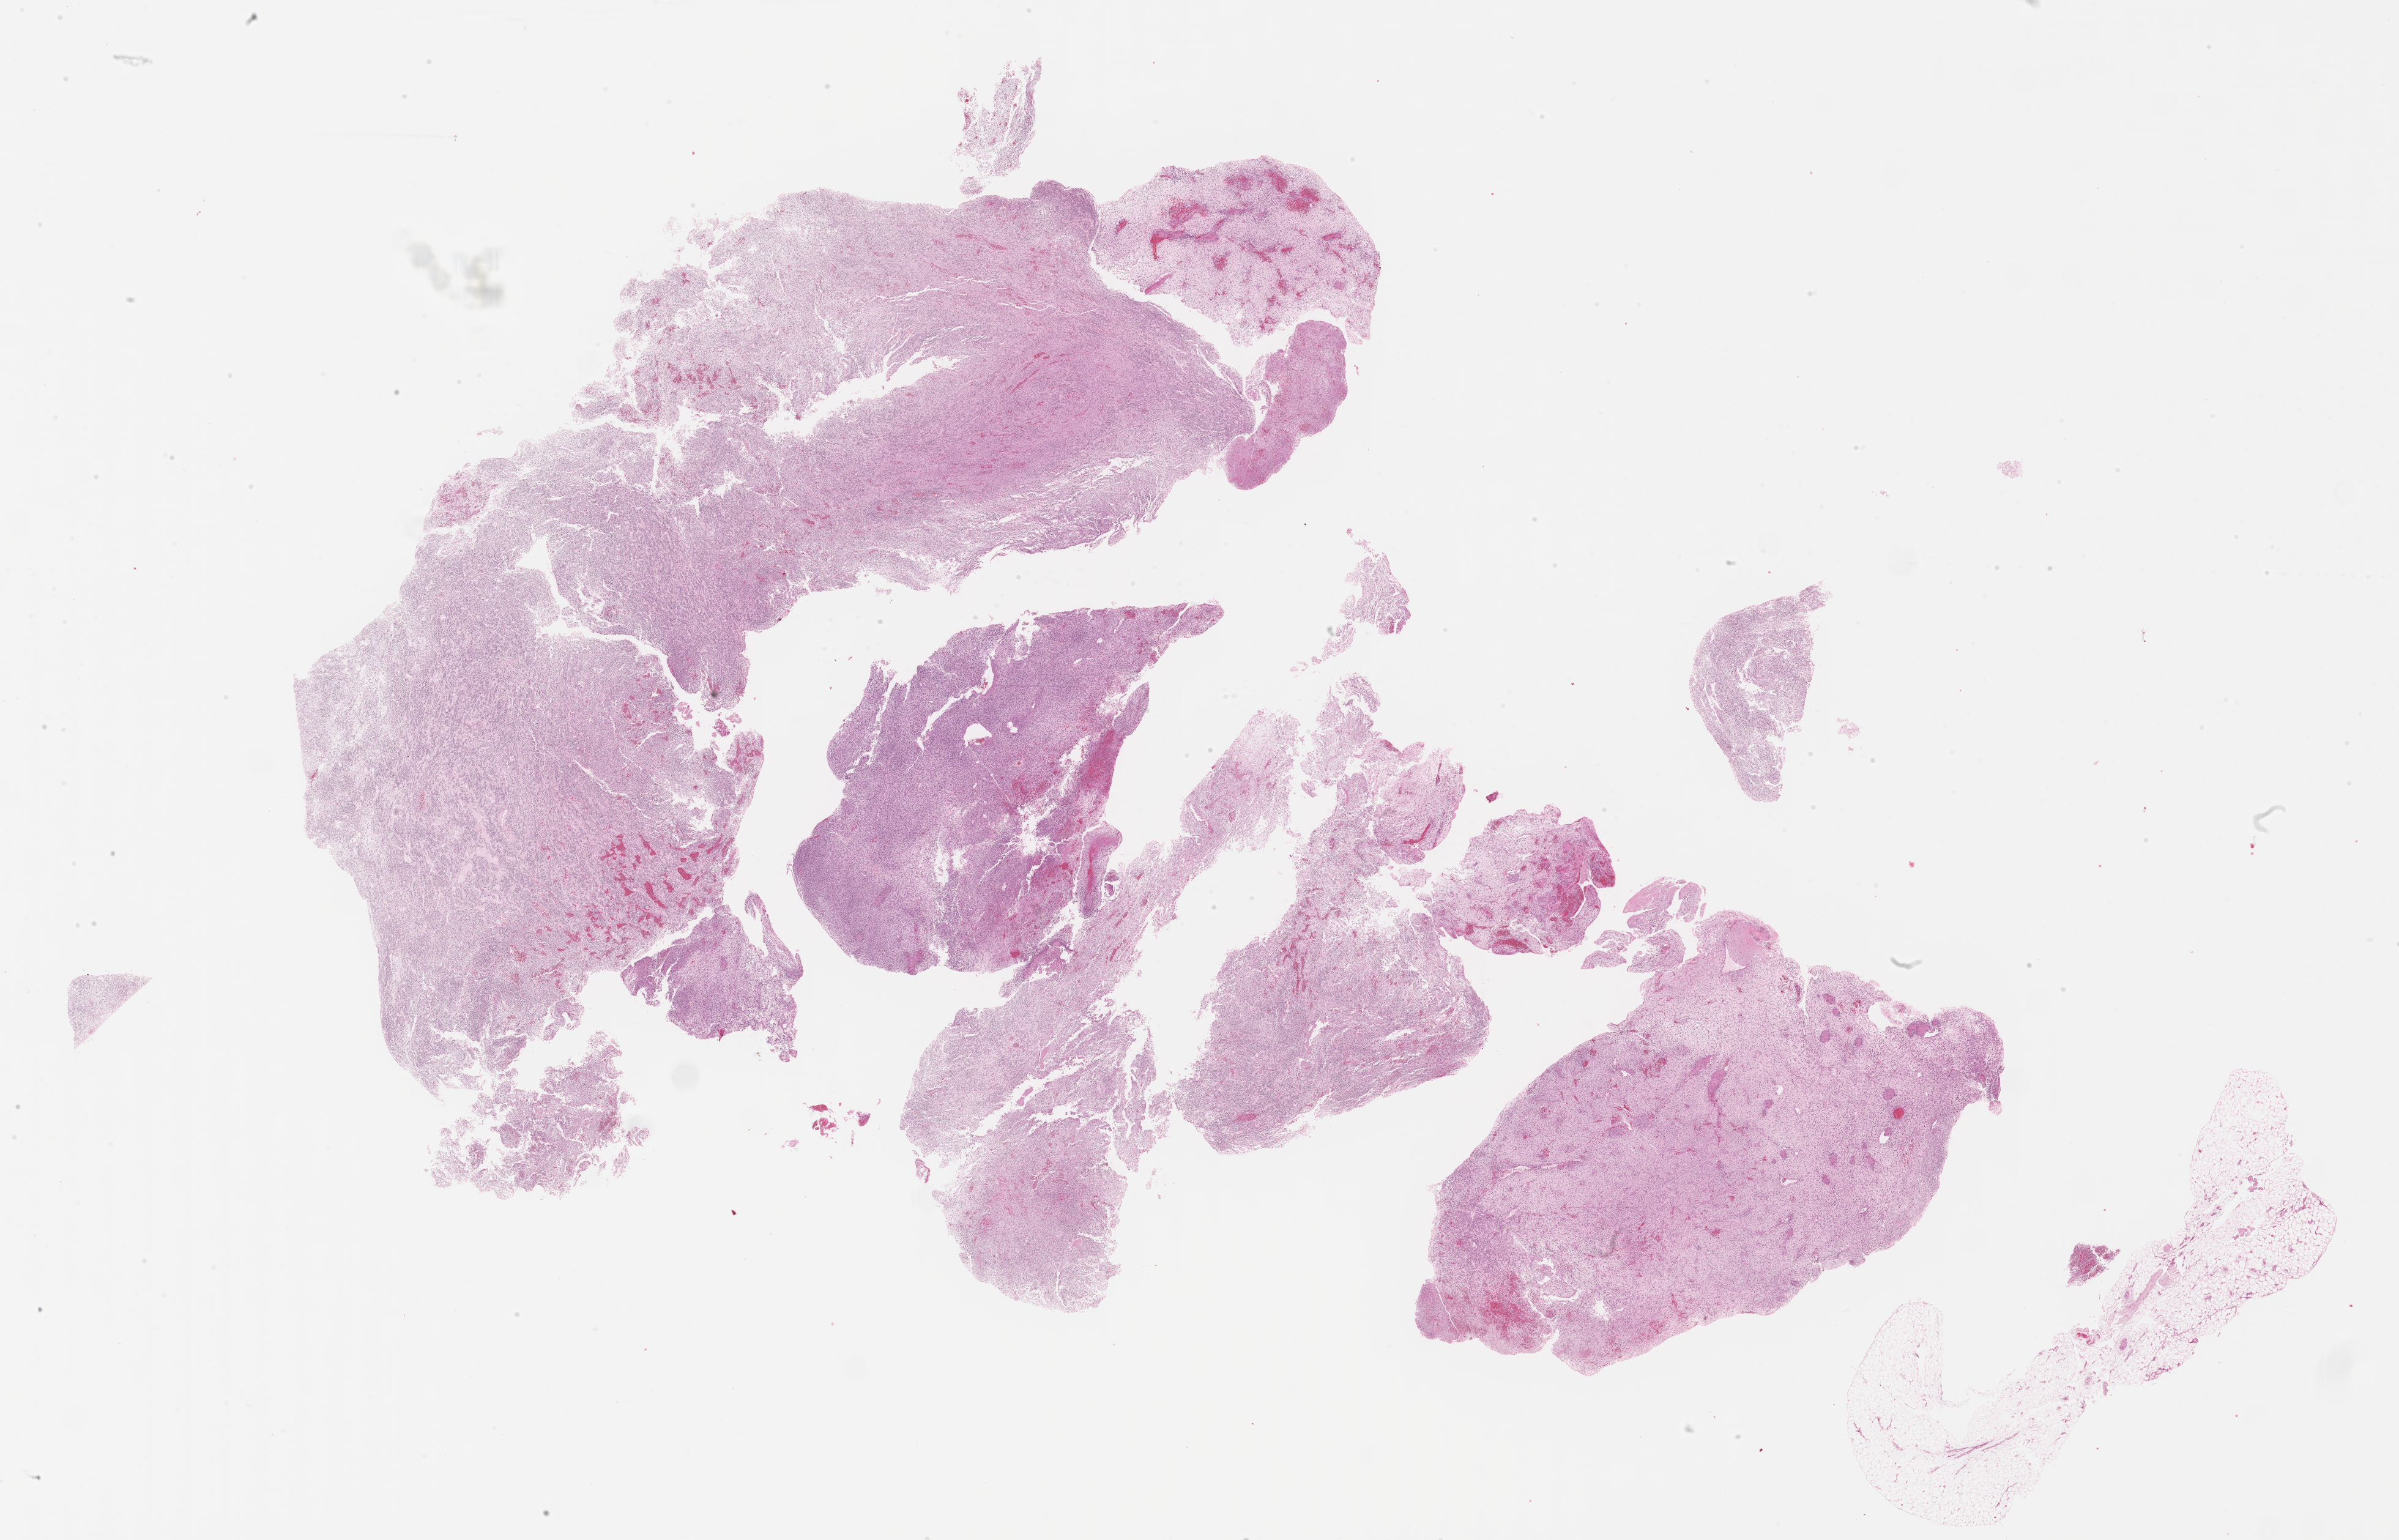
Hematoxylin and eosin (H&E) whole-slide image of tumor tissue, low-resolution overview of the scanned area, about 31.7 x 20.3 mm, formalin-fixed, paraffin-embedded (FFPE) tissue, sample anatomic site: bone, temporal-left (infratemporal fossa). Female patient, age at diagnosis 11.1 years.
Diagnosis: rhabdomyosarcoma; histological classification: embryonal rhabdomyosarcoma.